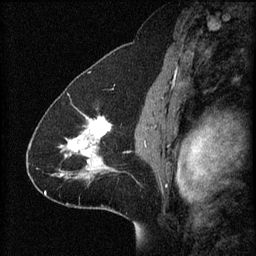
Breast MRI (dynamic contrast-enhanced), one sagittal slice. Slice 40 of 60 in the series (ordered by position). 3 images stored at this slice position (order not interpretable as contrast timing). 1.5 T. TE 4.2 ms, TR 8.2 ms. 256 × 256 image matrix, field of view 200 × 200 mm. Female patient, age 41 years.
Outlined on this slice (semi-automatic segmentation, software-assisted and operator-edited):
- analysis volume of interest (the breast-tissue region the enhancement analysis was run in; not a lesion): box from (x=59, y=112) to (x=118, y=181) px
- tumour enhancement mask (voxels above the 70 % enhancement threshold inside the analysis volume of interest): (x=60, y=116)–(x=114, y=179)